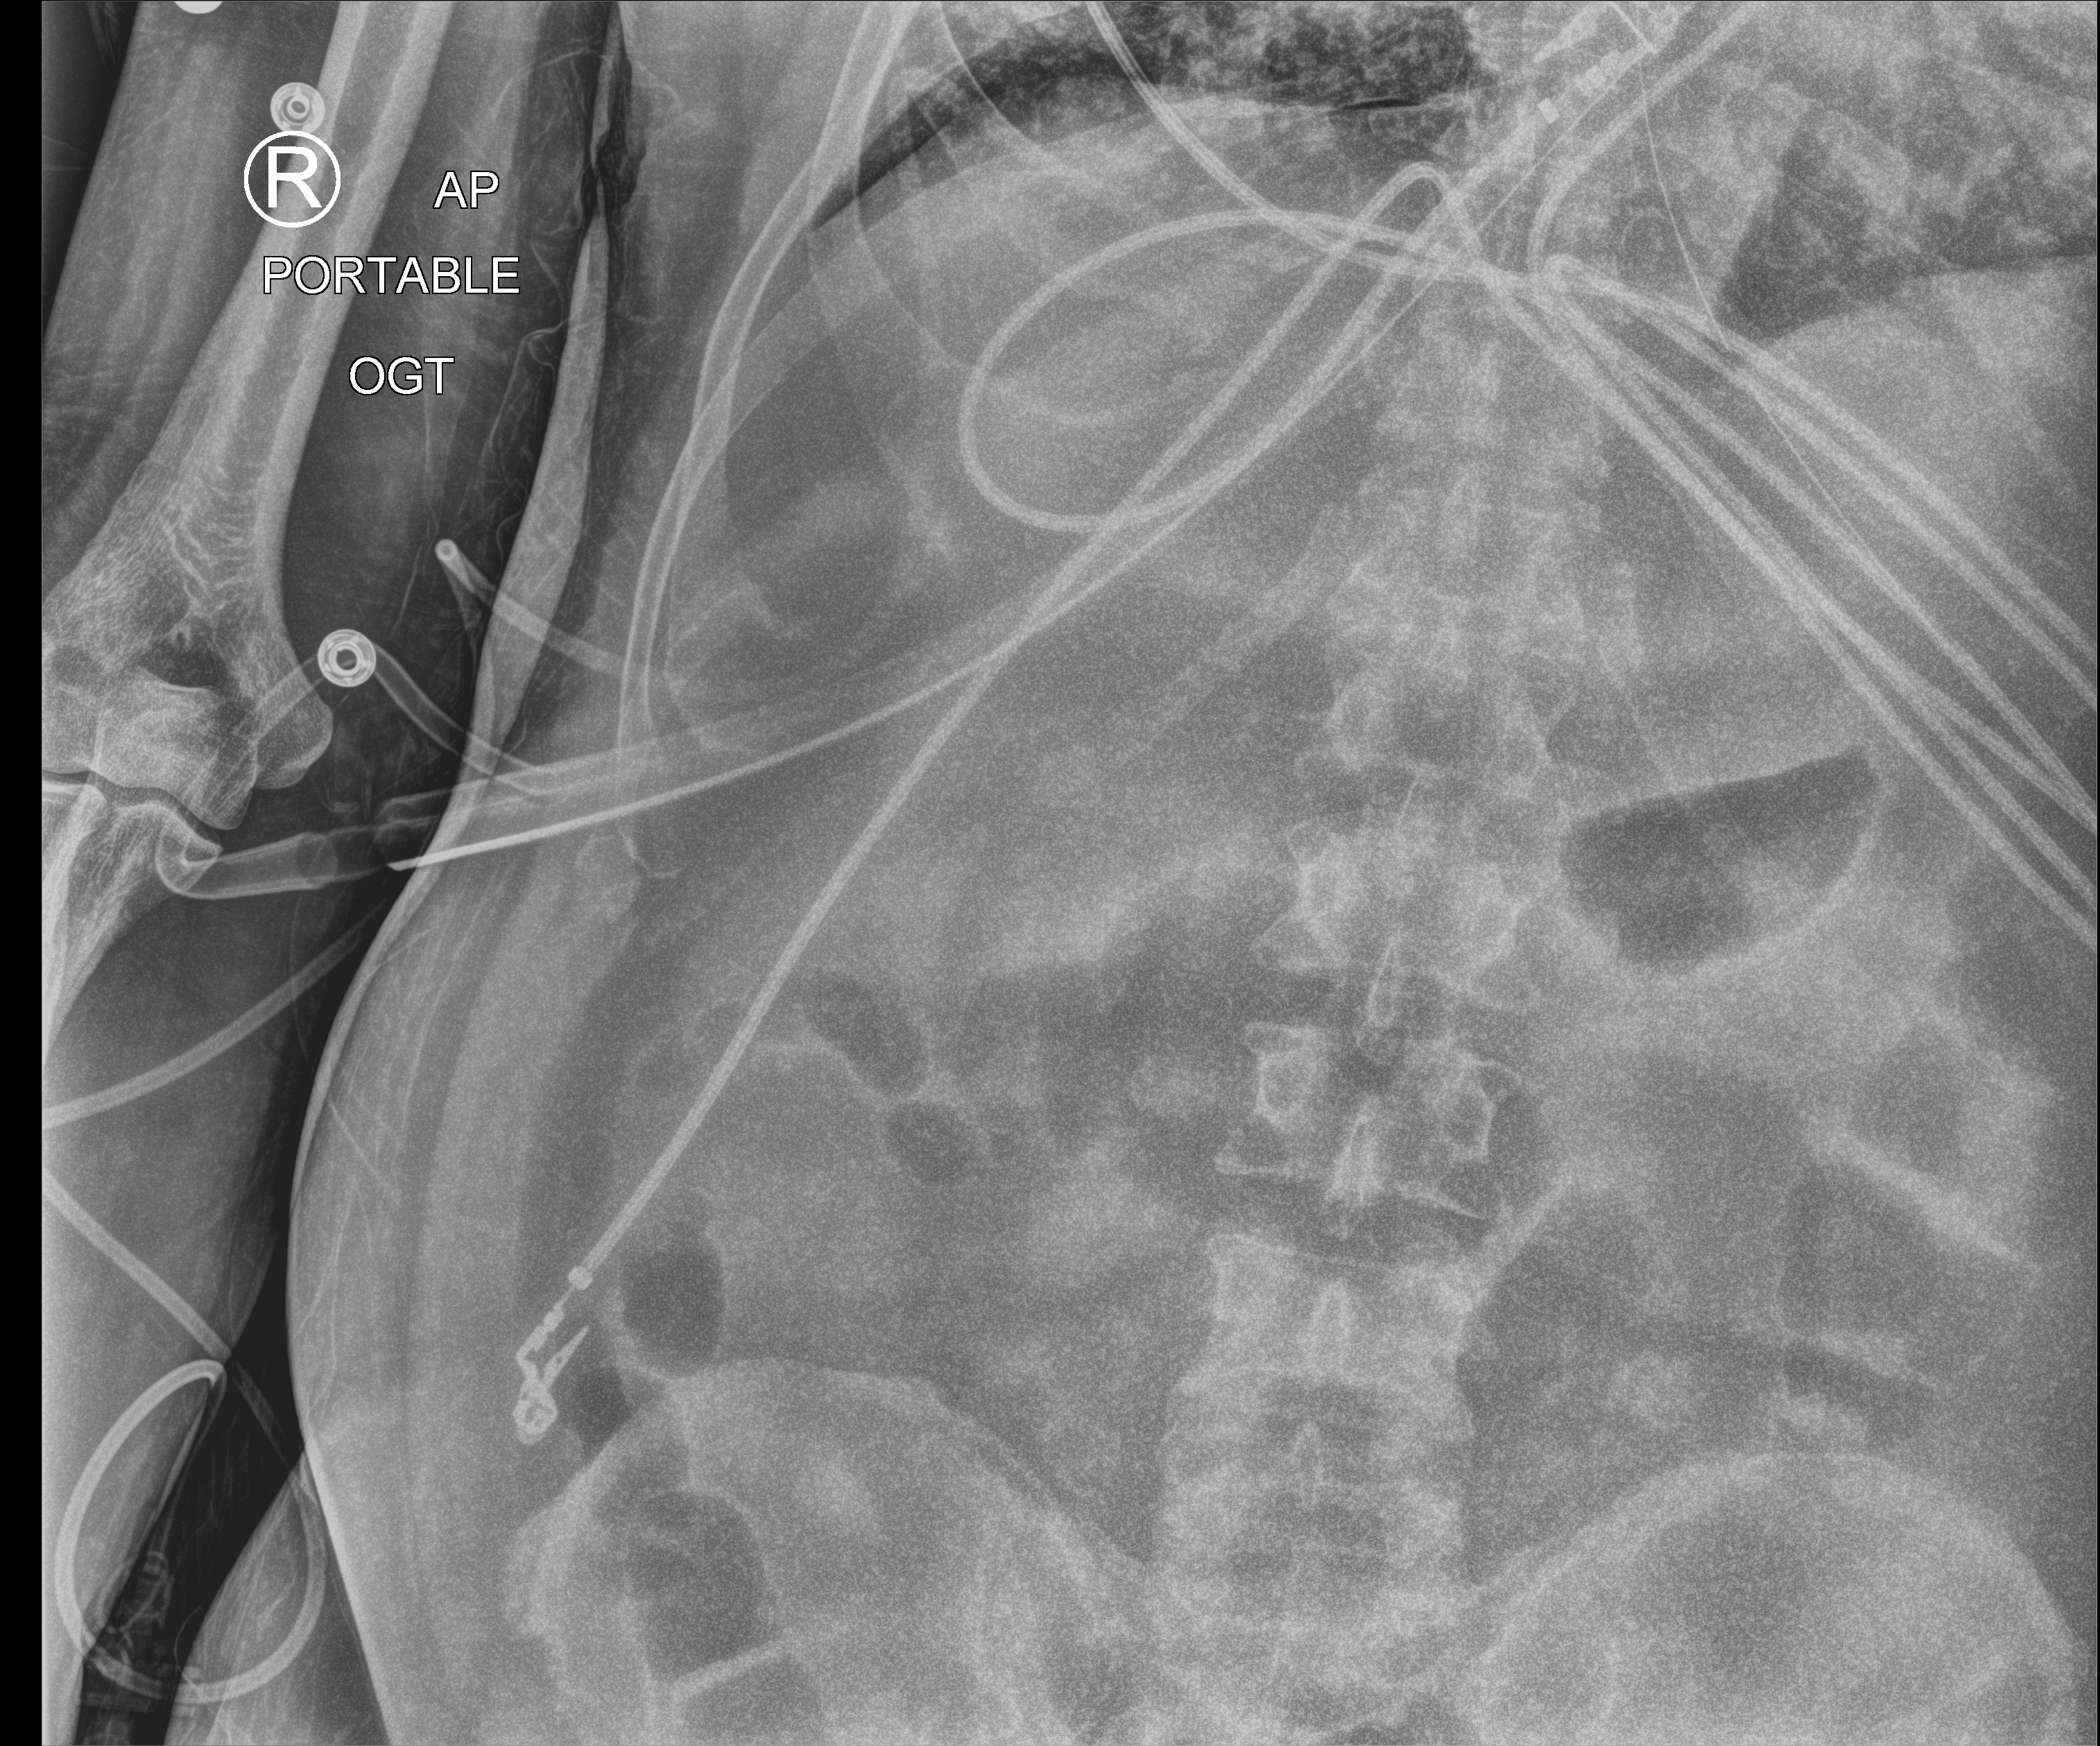
Bedside chest radiograph (computed radiography); anteroposterior (AP) projection. Male patient hospitalised with COVID-19, age 18–59 years.
From the hospital-stay record, not from the radiograph (when in the stay this image was taken is not recorded): mechanically ventilated during this hospital stay: yes.